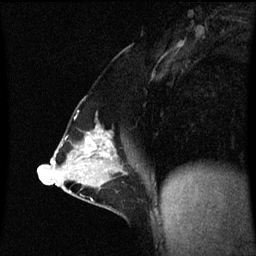
Breast MRI (dynamic contrast-enhanced), one sagittal slice. Dynamic contrast-enhanced series, image 2 of 3 at this slice position (ordered by acquisition). 1.5 T. TE 4.2 ms, TR 8.9 ms. 2 mm slice thickness. 256 × 256 image matrix, field of view 200 × 200 mm. Female patient, age 47 years. Case-level facts recorded for this patient, not image findings: setting: breast cancer imaged before/during neoadjuvant chemotherapy; receptor status: HR-positive, HER2-negative.
Annotated regions visible in this slice (semi-automatic segmentation, software-assisted and operator-edited):
- analysis volume of interest (the breast-tissue region the enhancement analysis was run in; not a lesion): bounding box (x1, y1, x2, y2) in pixels: (53, 112, 130, 209)
- tumour enhancement mask (voxels above the 70 % enhancement threshold inside the analysis volume of interest): (85, 126, 116, 159)